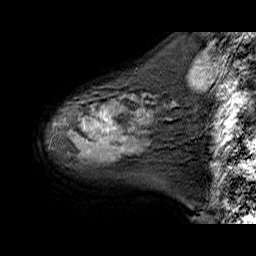
Breast MRI (dynamic contrast-enhanced), one sagittal slice; dynamic contrast-enhanced series, time point 2 of 6 at this slice position (early post-contrast); 1.5 T; TE 6.3 ms, TR 32.9 ms; 4 mm slice thickness; 256 × 256 image matrix, field of view 200 × 200 mm. Female patient. From the clinical record (not read from this slice): setting: breast cancer imaged before/during neoadjuvant chemotherapy; receptor status: HER2-positive.
Outlined on this slice (semi-automatic segmentation, software-assisted and operator-edited):
- analysis volume of interest (the breast-tissue region the enhancement analysis was run in; not a lesion): bounding box <55,92,177,162> (left, top, right, bottom; pixels)
- tumour enhancement mask (voxels above the 100 % enhancement threshold inside the analysis volume of interest): <97,112,110,131>